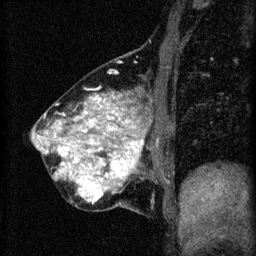
Breast MRI (dynamic contrast-enhanced), one sagittal slice; slice 19 of 60 in the series (ordered by position); 3 images stored at this slice position (order not interpretable as contrast timing); 1.5 T; TE 4.2 ms, TR 8.2 ms; 2 mm slice thickness; 256 × 256 image matrix, field of view 180 × 180 mm. Patient: female, 40 years.
Structures marked on this image (semi-automatically segmented with operator editing):
- analysis volume of interest (the breast-tissue region the enhancement analysis was run in; not a lesion): bounding box <32,80,173,213> (left, top, right, bottom; pixels)
- tumour enhancement mask (voxels above the 70 % enhancement threshold inside the analysis volume of interest): <44,96,145,203>